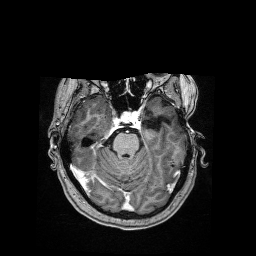
Brain MRI from a brain-tumour surgery series, one axial slice. Position 109 of 176 along the scan axis. T1-weighted post-contrast. 1.2 mm slice thickness. 256 × 256 image matrix, field of view 256 × 256 mm. From the clinical record (not read from this slice): histopathology: Dysembryoplastic neuroepithelial tumor; WHO grade: 1; IDH mutation: no; tumour location: Left Temporal.
Structures marked on this image (outlined manually by an expert reader):
- tumour: box from (x=148, y=113) to (x=152, y=117) px